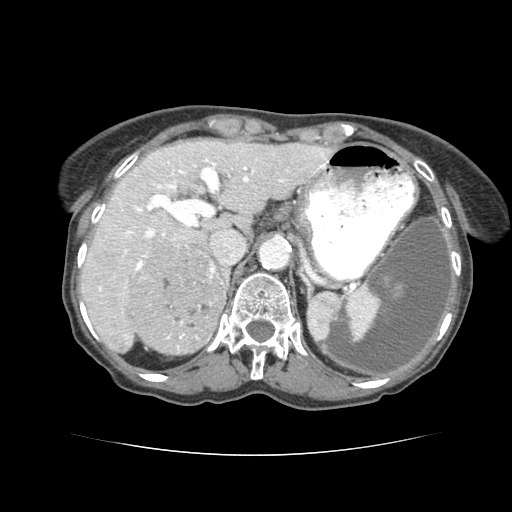
Contrast-enhanced abdominal CT (liver protocol), one axial slice; slice 52 of 77 in the series (ordered by position); reconstruction kernel STANDARD; soft-tissue window (W 400 / L 40 HU); 2.5 mm slice thickness; 512 × 512 image matrix, field of view 340 × 340 mm. Case-level facts recorded for this patient, not image findings: diagnosis: hepatocellular carcinoma (patient treated with transarterial chemoembolisation; whether this scan precedes or follows treatment is not stated here); TNM stage (as recorded): Stage-I; Child-Pugh class: A; tumour nodularity: uninodular; tumour size: 7.6 cm.
Structures marked on this image (semi-automatically segmented with operator editing):
- liver parenchyma outside the tumour (the mass and vessels are separate outlines, so this box may not span the whole liver): box from (x=76, y=136) to (x=322, y=345) px
- mass: (x=129, y=242)–(x=225, y=354)
- liver vessels: (x=129, y=158)–(x=279, y=330)